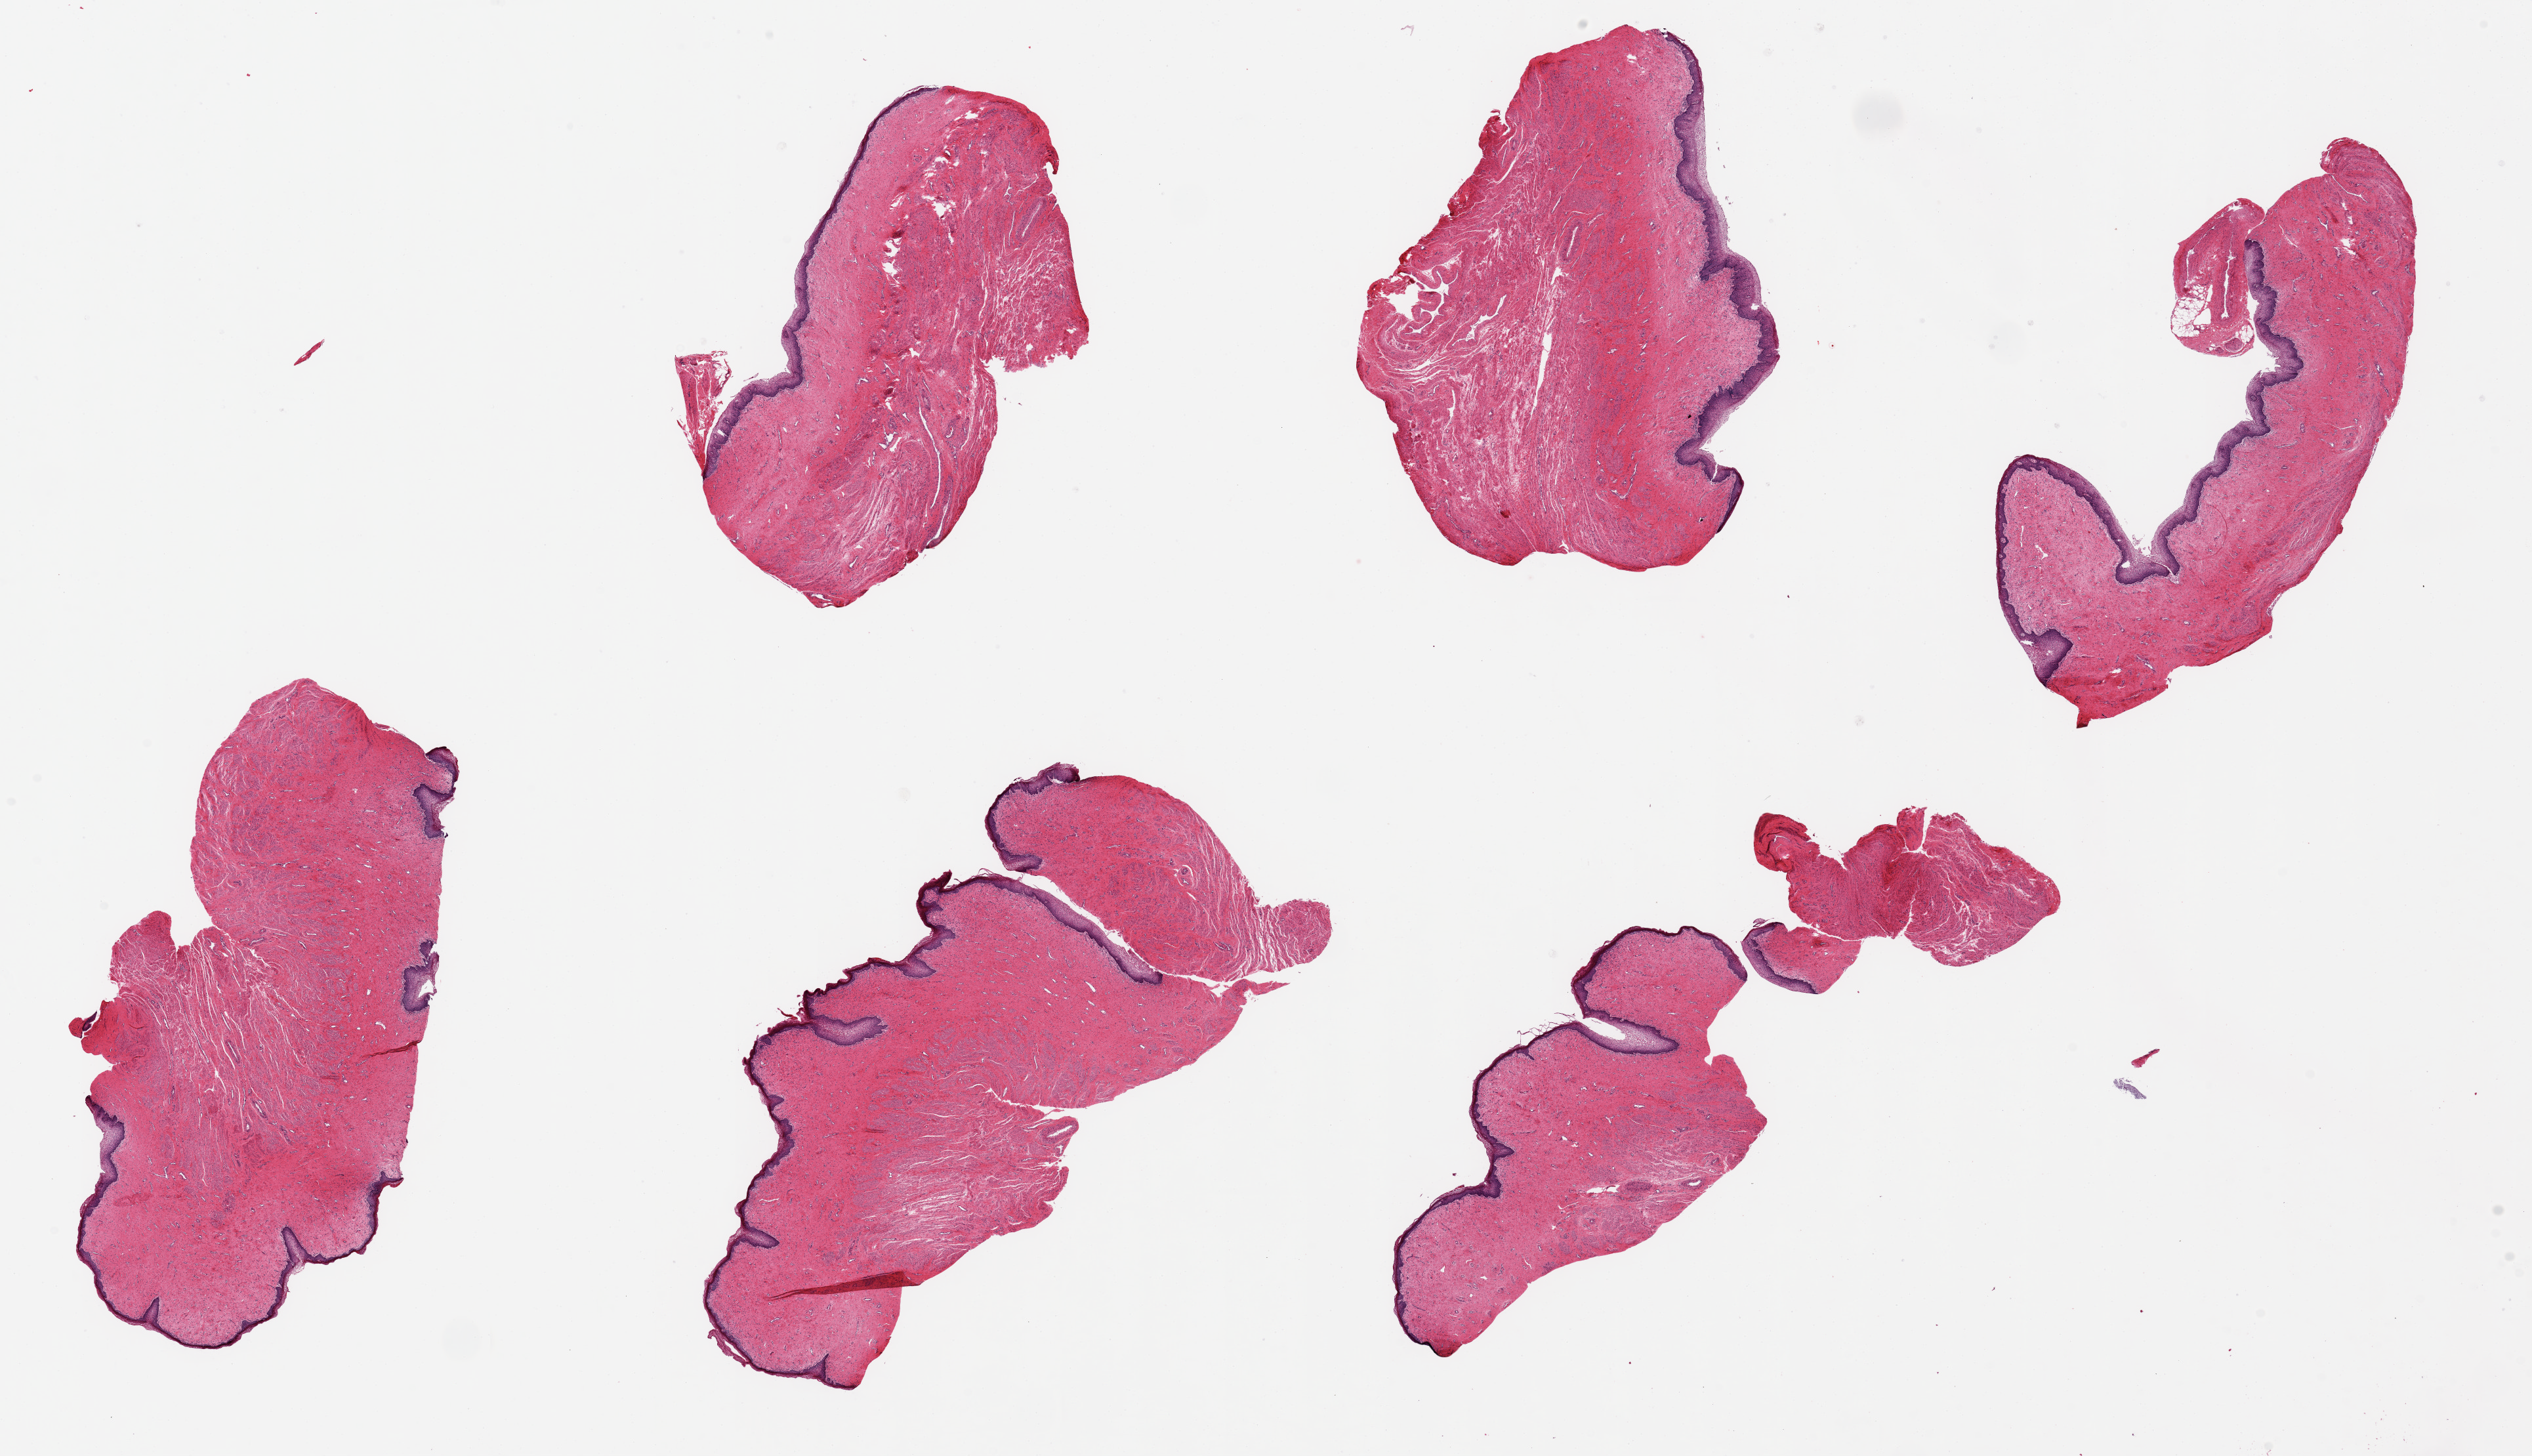
Haematoxylin and eosin whole-slide image, brightfield — whole scanned area (about 30.5 x 17.5 mm, from a 20x scan) shown as a low-resolution overview; PAXgene-fixed, paraffin-embedded tissue; section of vagina (target tissue); donor tissue sample. Female donor.
Review note (as recorded): 6 pieces up to 8x4 mm; well preserved mucosa on all pieces.